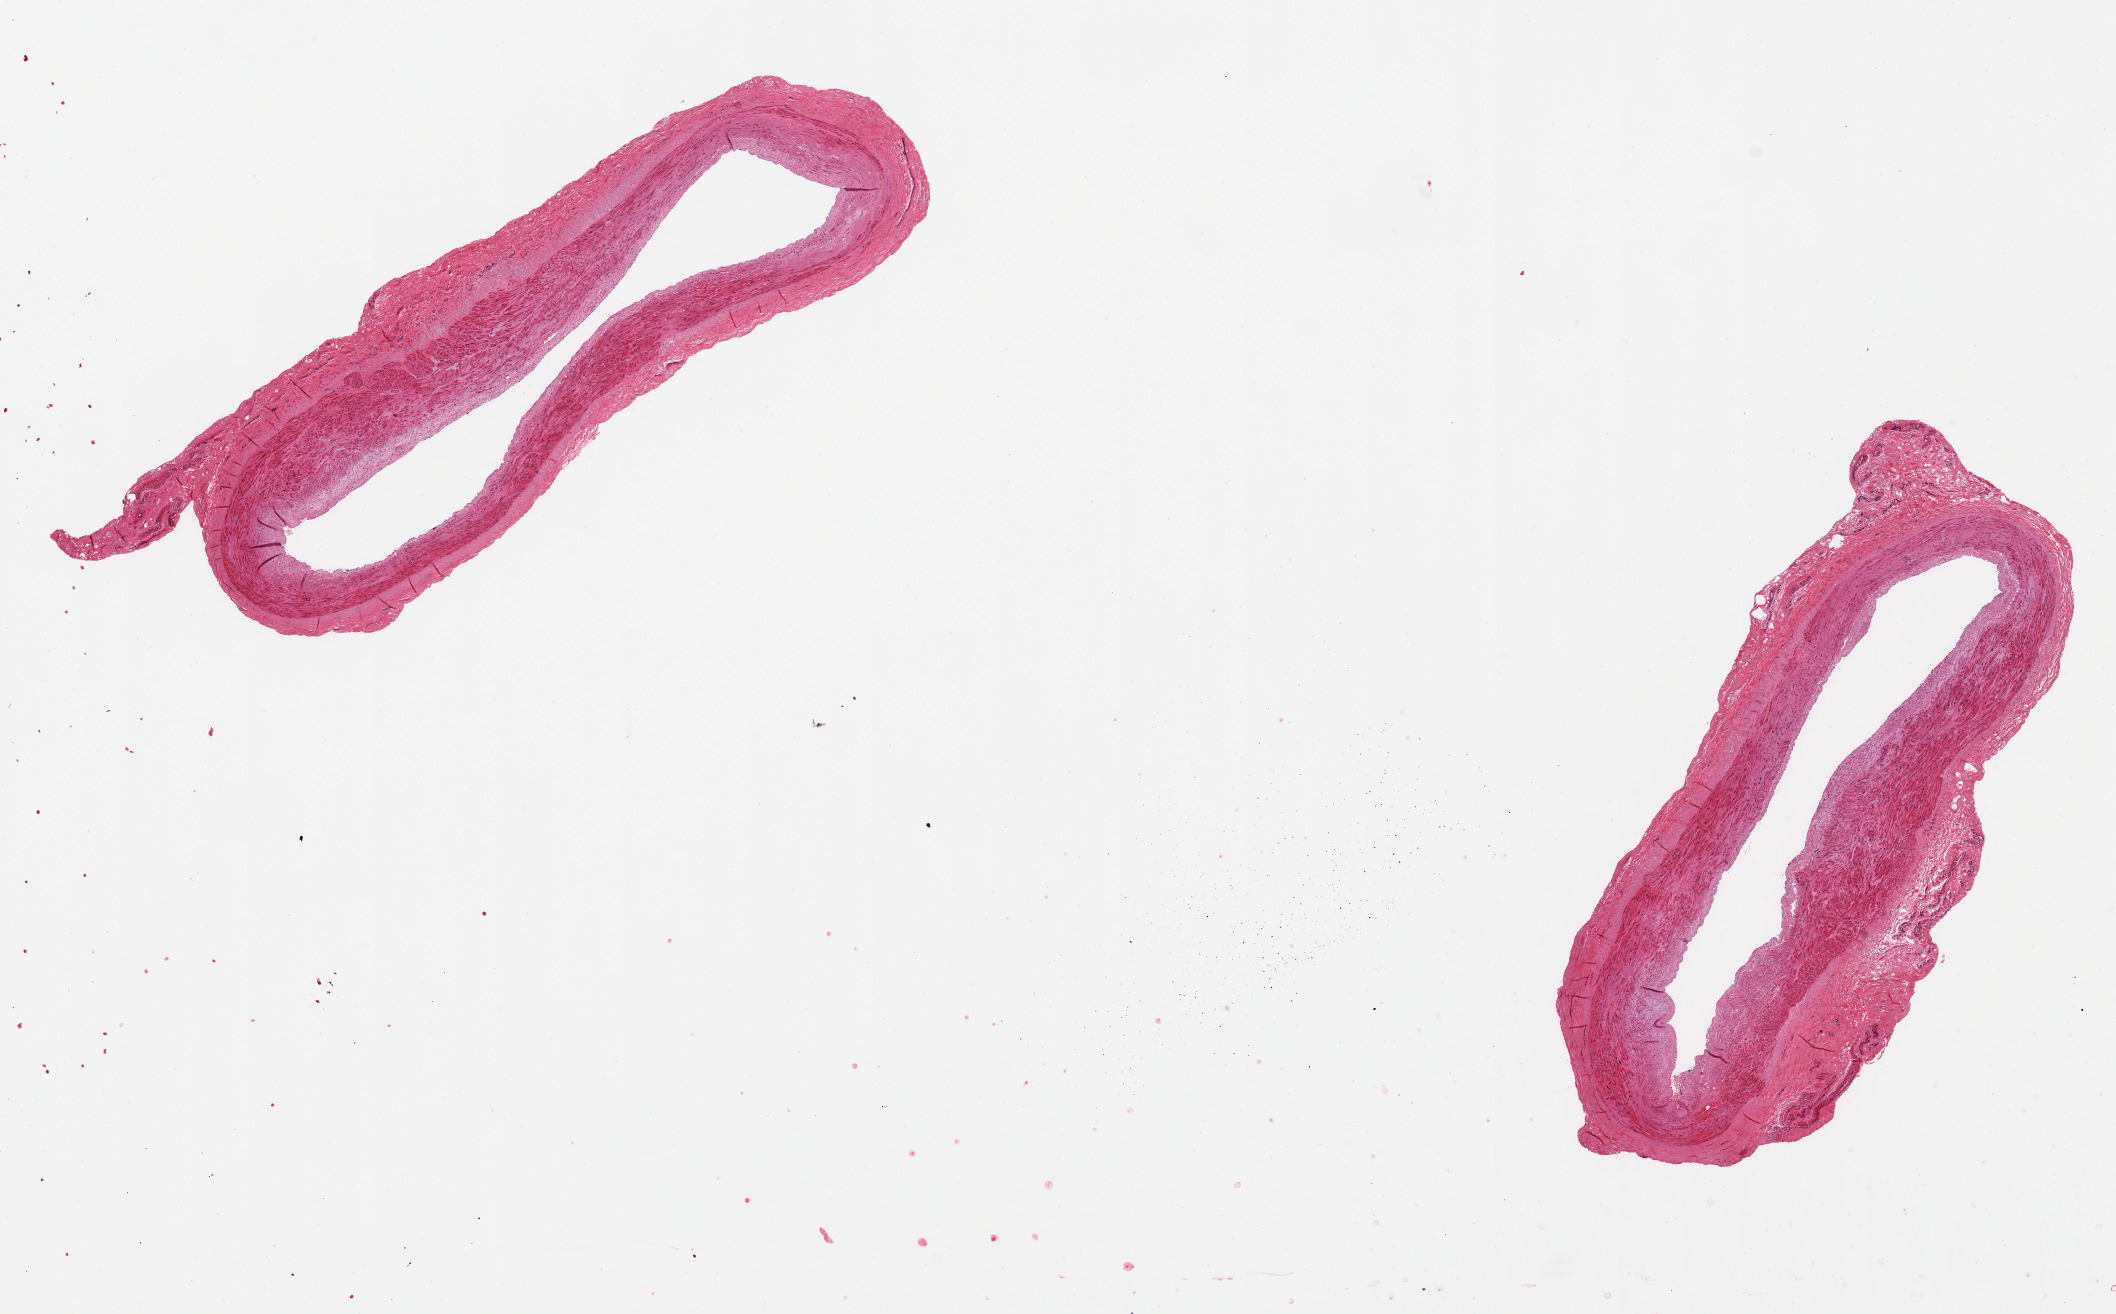
Haematoxylin and eosin whole-slide image — a low-resolution overview of the entire scanned area, about 16.7 x 10.4 mm, PAXgene-fixed paraffin-embedded (PFPE) section, section of tibial artery (target tissue), donor tissue sample.
* reviewer comment on this tissue sample: Minimal sclerosis. Two sections. 6 x 2.5mm